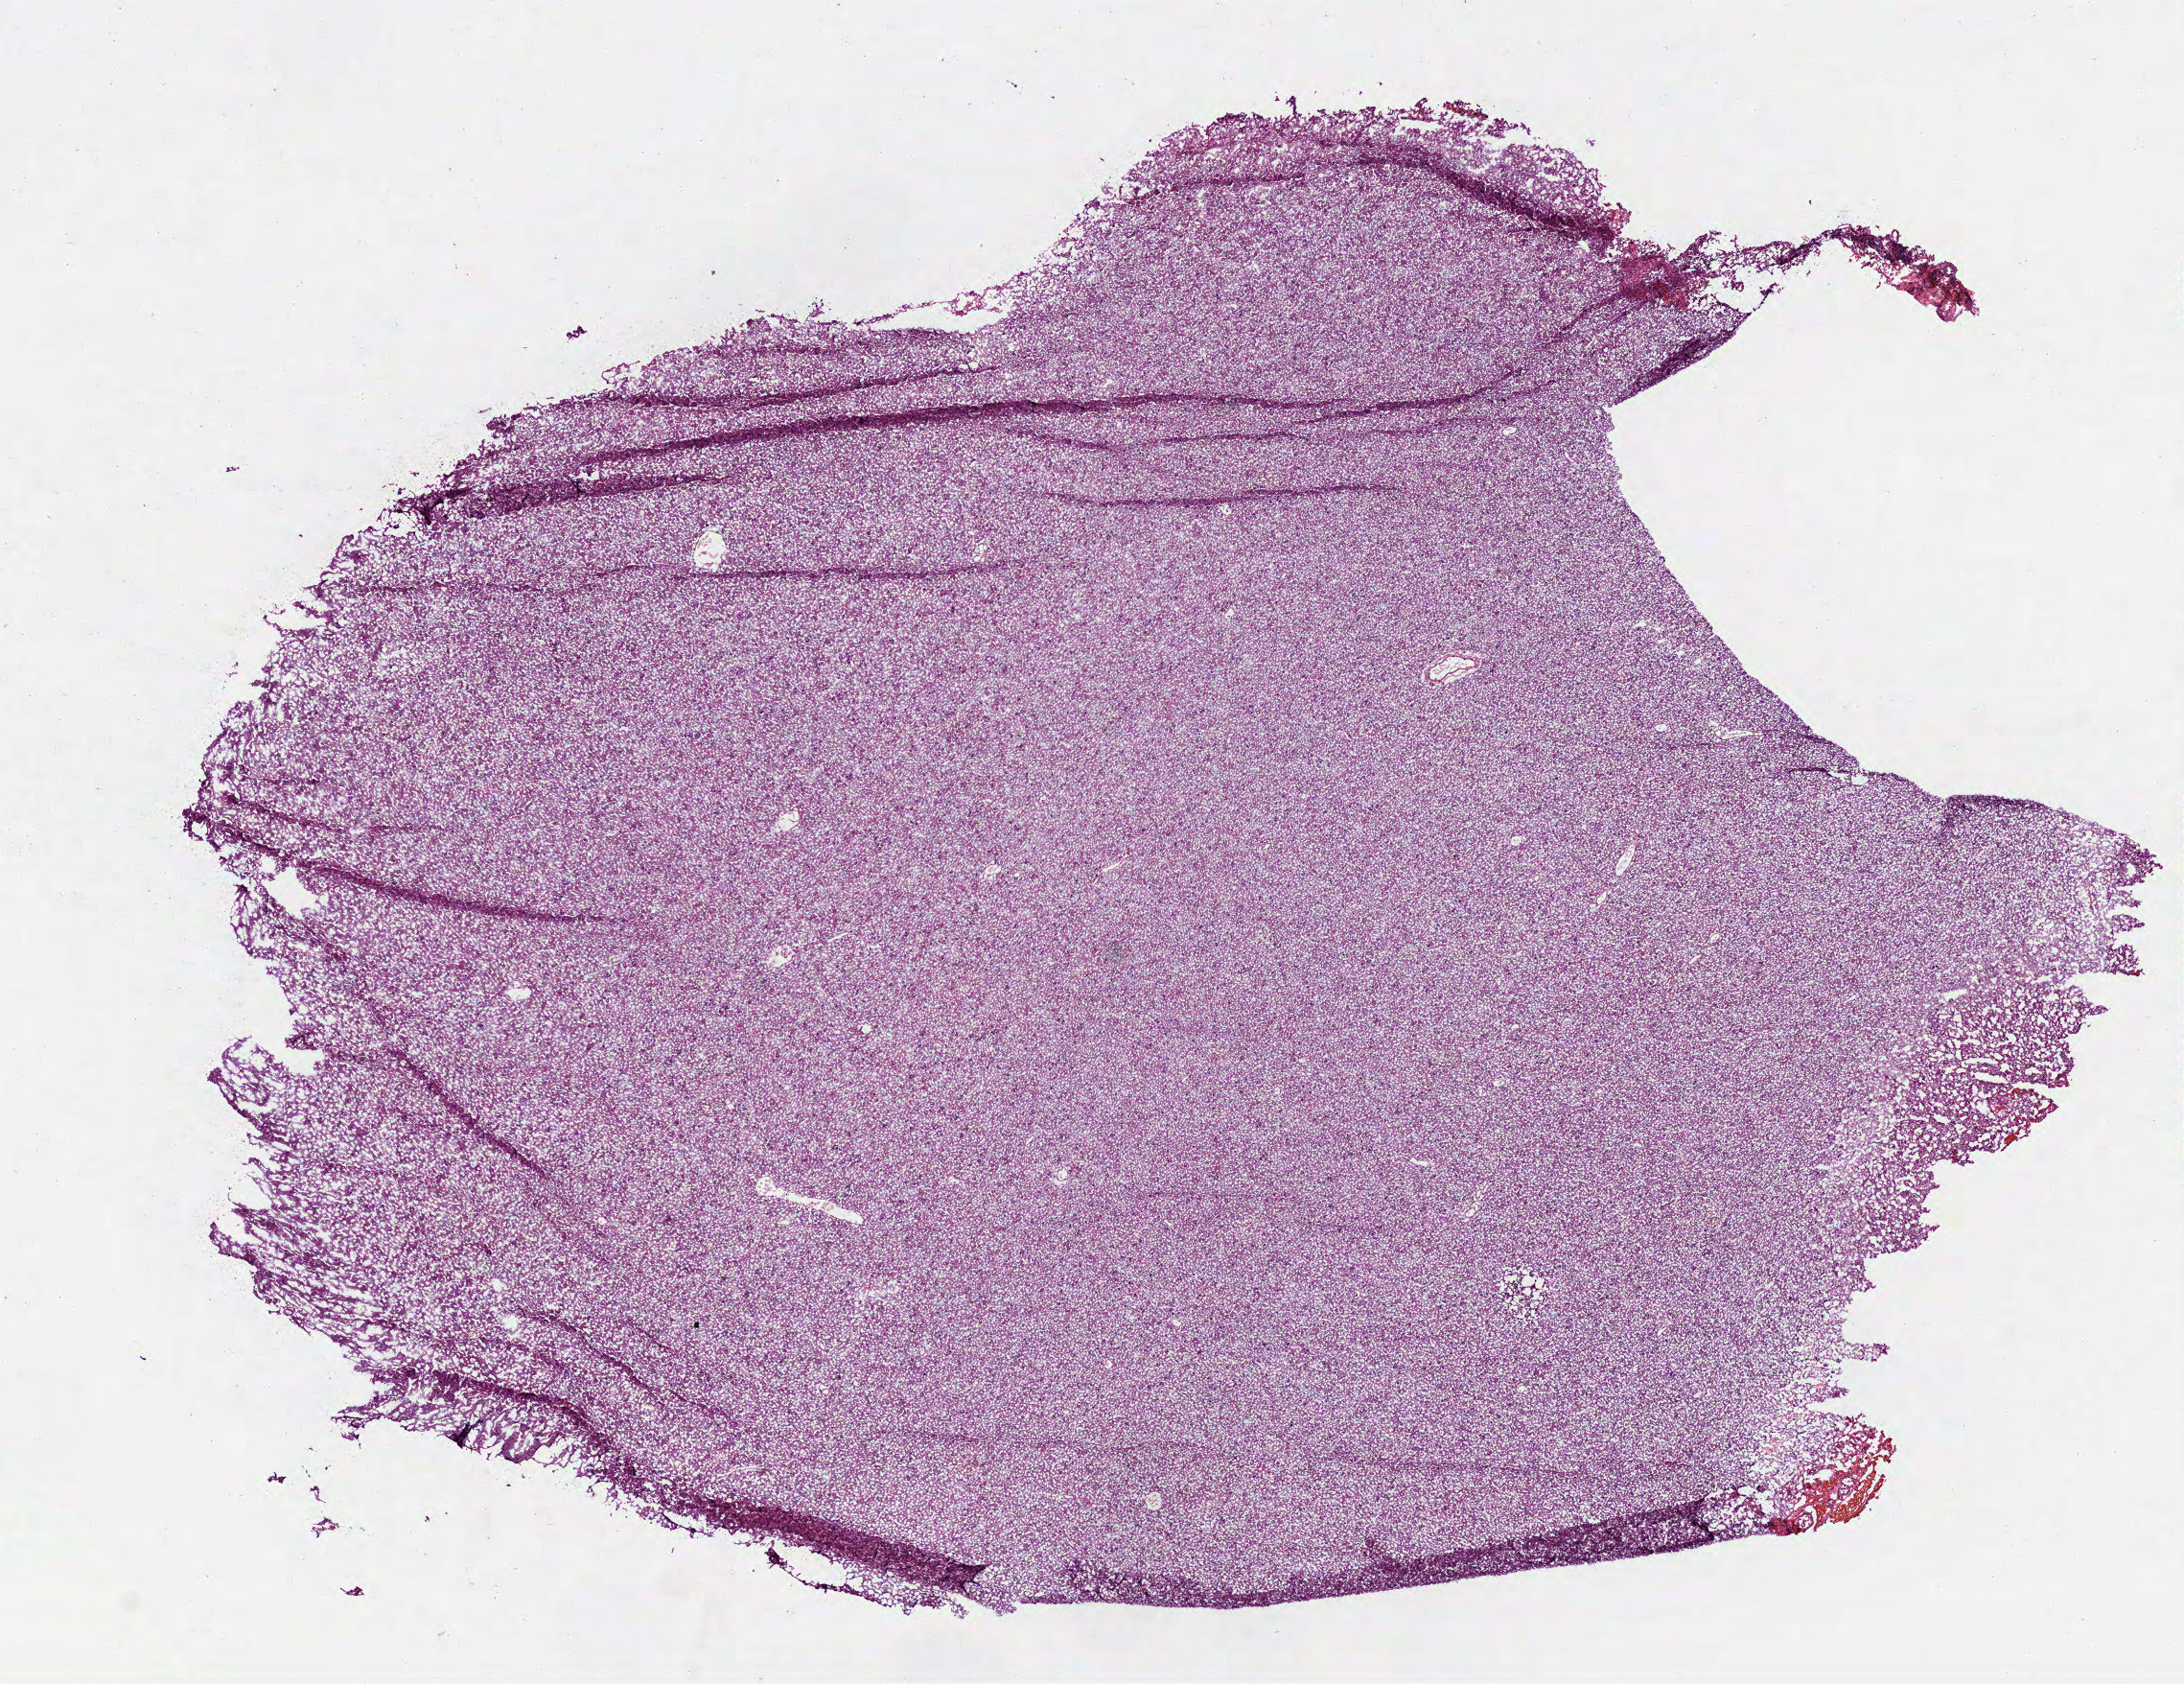
Whole-slide histology image, H&E-stained — a low-resolution overview of the entire scanned area, about 9.2 x 7.1 mm; frozen section from the bottom of the tissue portion; sample: primary tumour, brain. Male patient; age at initial diagnosis 52 years.
Diagnosis: Mixed glioma (cerebrum).